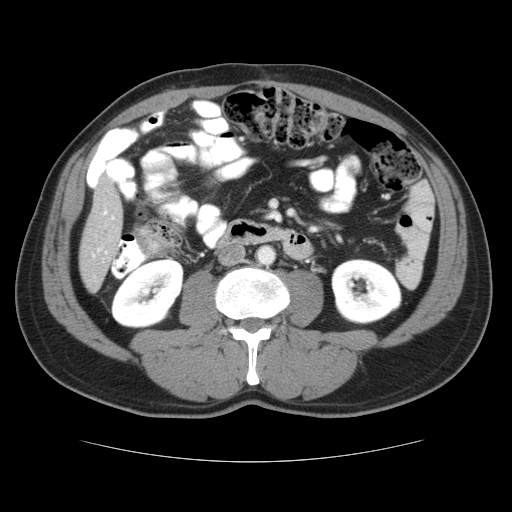
Contrast-enhanced abdominal CT, one axial slice; slice 9 of 37 in the series (ordered by position); reconstruction kernel STANDARD; intravenous contrast given; soft-tissue window (W 400 / L 40 HU); 5 mm slice thickness; 512 × 512 image matrix, field of view 374 × 374 mm. Male patient, age 66 years. Case-level facts recorded for this patient, not image findings: diagnosis: colorectal cancer liver metastases, imaged before liver resection; multiple liver metastases: yes; largest metastasis: 1.6 cm; disease in both lobes: yes.
Structures marked on this image (outlined manually by an expert reader):
- hepatic veins: bounding box <92,209,115,257> (left, top, right, bottom; pixels)
- liver: <80,174,124,291>
- planned liver remnant (the part of the liver to remain after resection): <80,175,124,292>
- liver metastasis: <100,227,109,236>